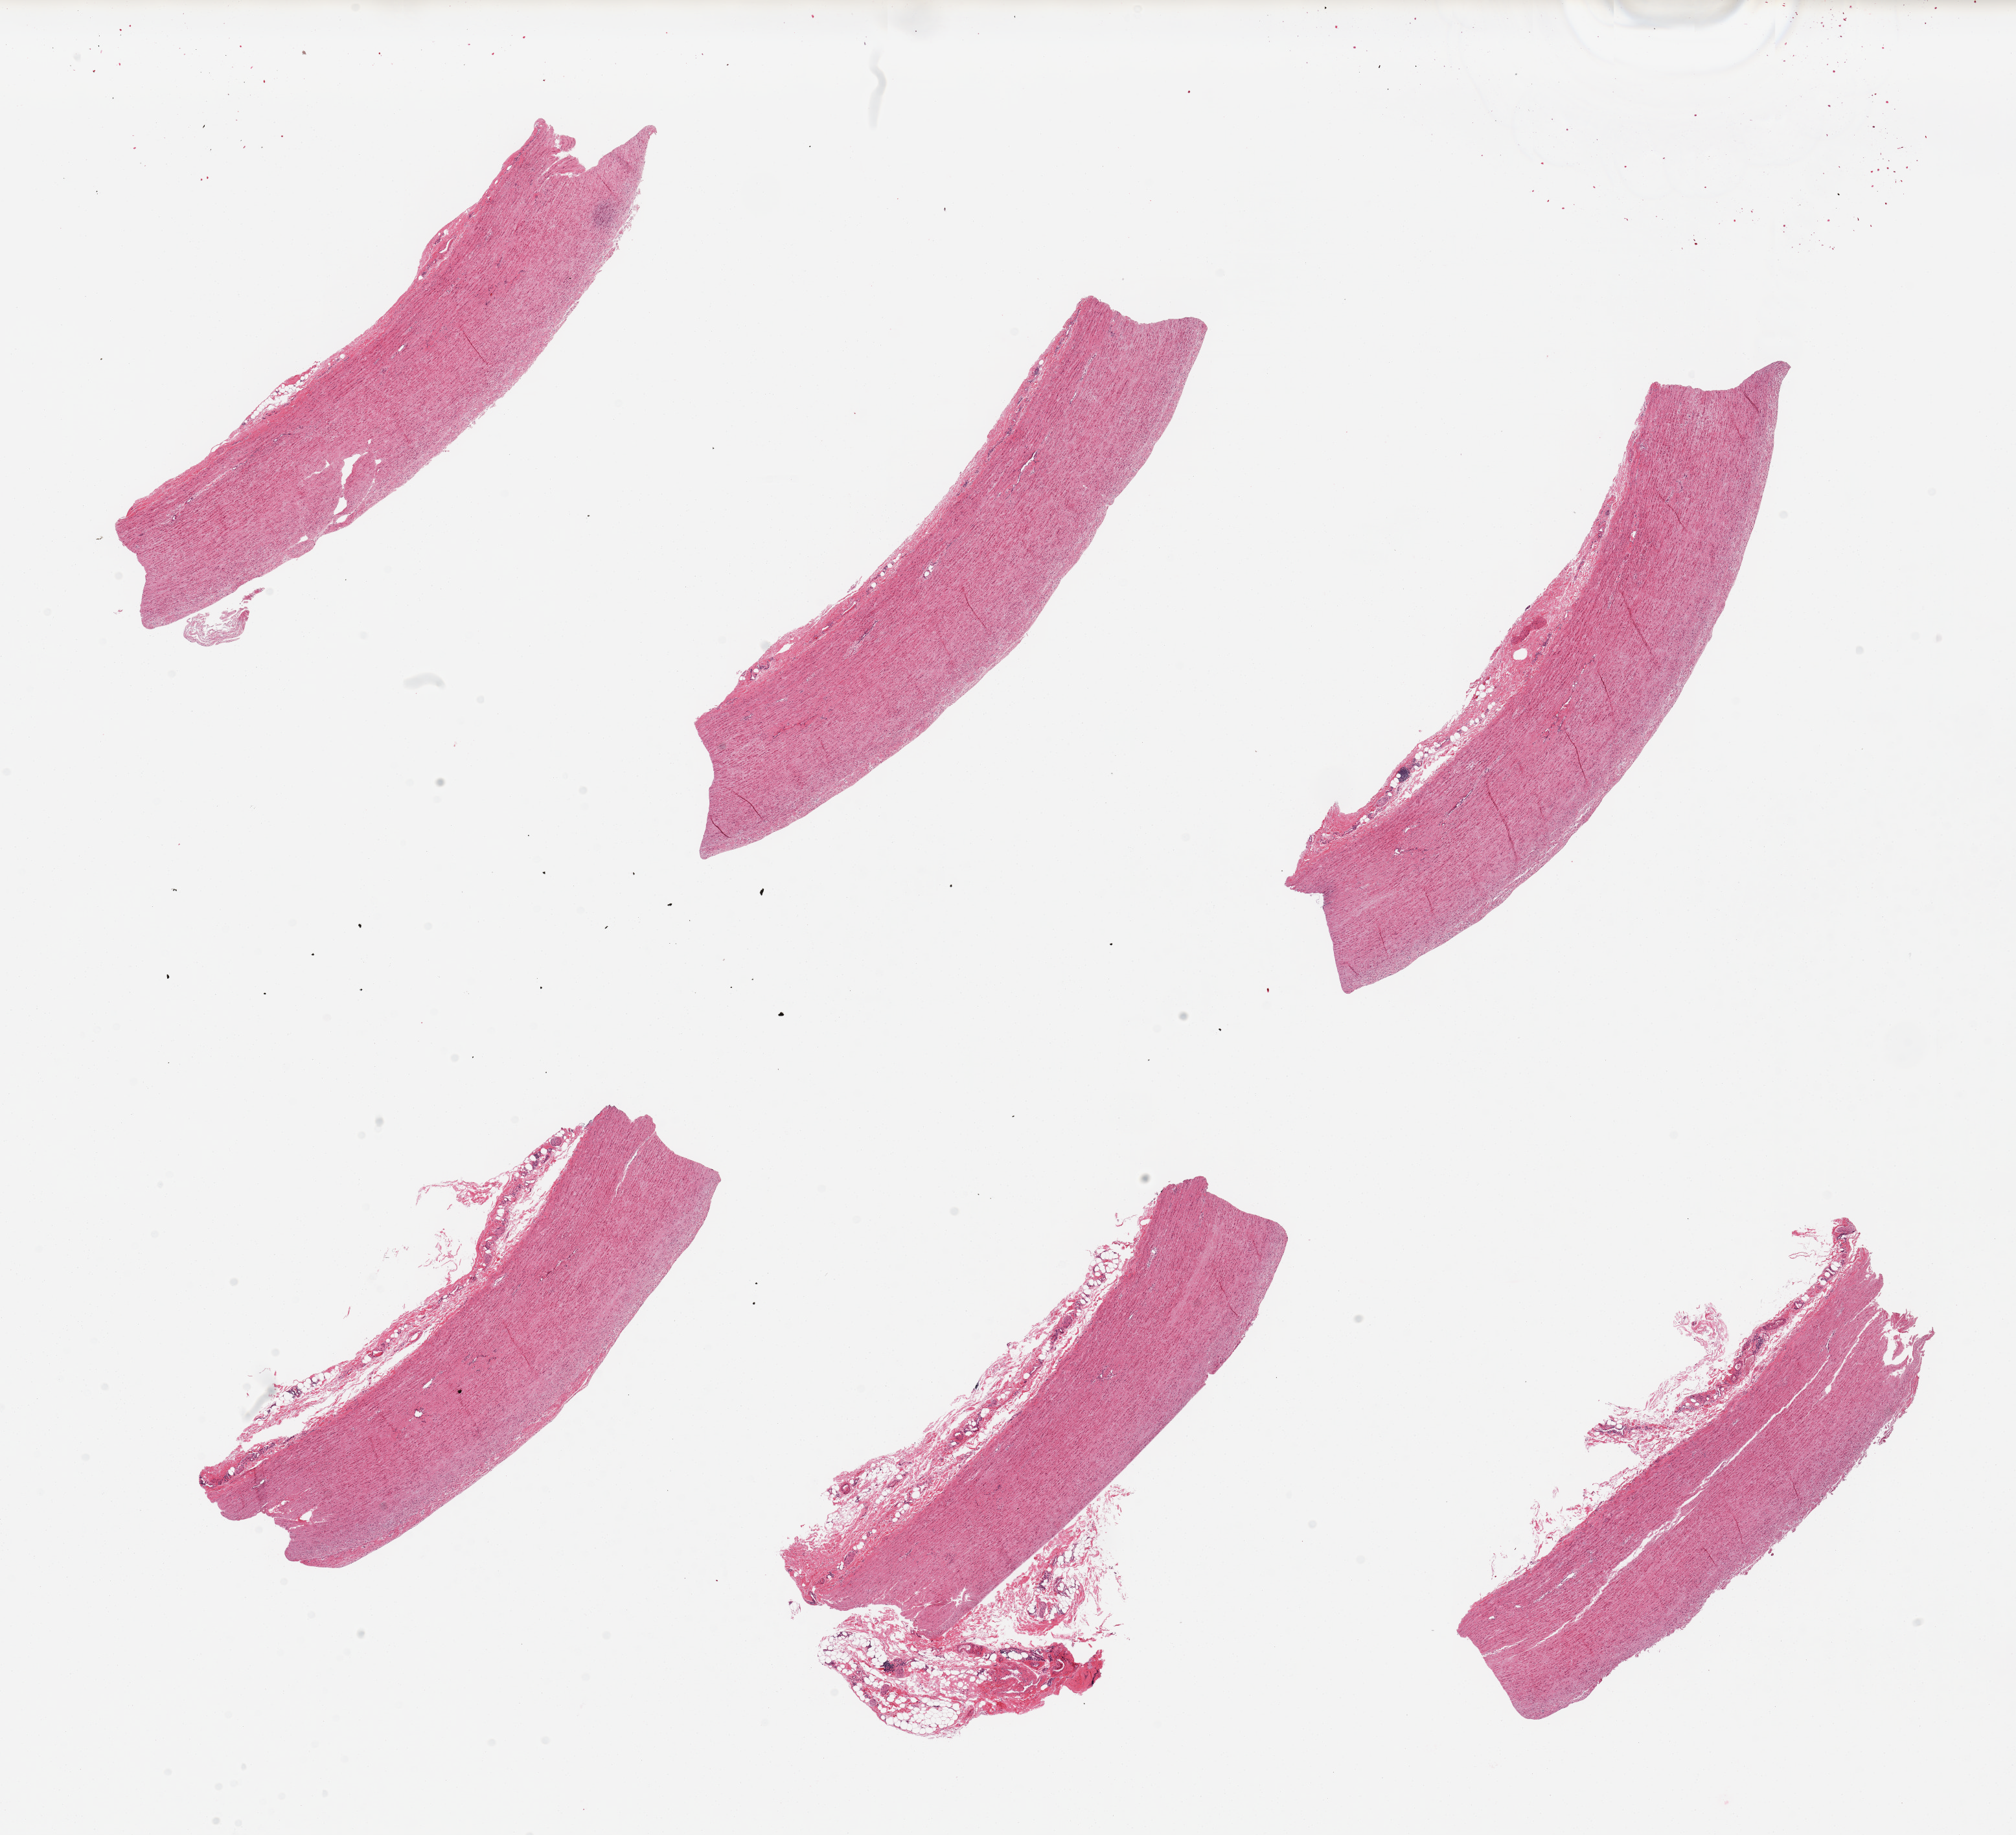
Hematoxylin and eosin (H&E) whole-slide image — shown as a low-resolution overview of the whole scanned area (about 24.6 x 22.4 mm, acquisition: 20x scan); PAXgene-fixed, paraffin-embedded tissue; target tissue: aorta; donor tissue sample. Donor: male.
* review note (as recorded): 6 pieces